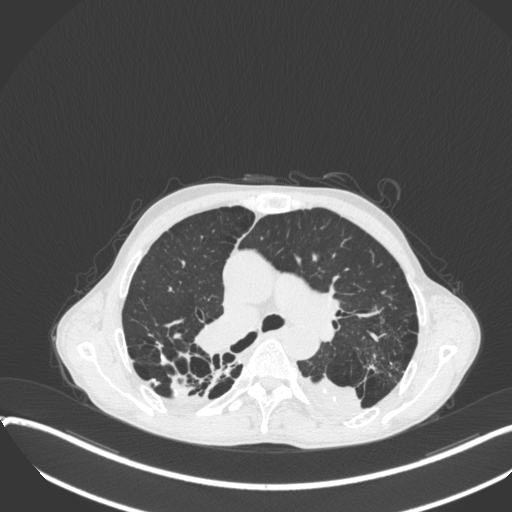
Chest CT, one axial slice; slice 246 of 400 in the series (ordered by position); reconstruction kernel B31f; lung window (W 1500 / L -600 HU); 1 mm slice thickness; 512 × 512 image matrix, field of view 400 × 400 mm. Male patient, age 57 years. Case-level facts recorded for this patient, not image findings: clinical TNM (as recorded): T4 N0 M0.
Annotated regions visible in this slice (bounding box drawn by a radiologist):
- lung tumour (recorded histology: squamous cell carcinoma): bounding box (x1, y1, x2, y2) in pixels: (298, 368, 365, 426)